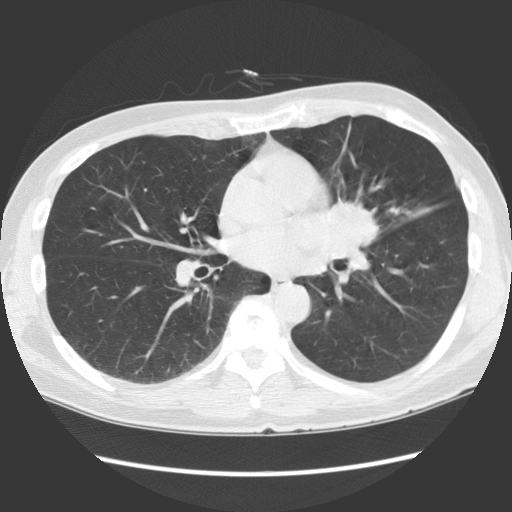
Low-dose screening chest CT, one axial slice; position 66 of 136 along the scan axis; reconstruction kernel STANDARD; 140 kVp; lung window (W 1500 / L -600 HU); 2.5 mm slice thickness; 512 × 512 image matrix.
Outlined on this slice (manually delineated by an expert):
- lesion 1 (tumor, hilum of left lung): bounding box (x1, y1, x2, y2) in pixels: (331, 199, 380, 247)